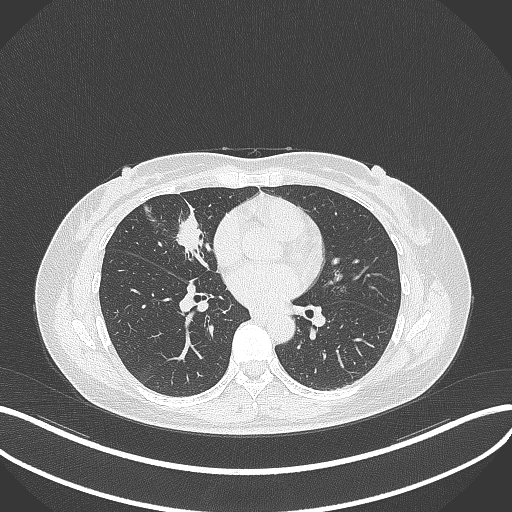
Chest CT, one axial slice; slice 139 of 284 in the series (ordered by position); reconstruction kernel B70f; lung window (W 1500 / L -600 HU); 512 × 512 image matrix, field of view 400 × 400 mm. Patient: female, 43 years. Case-level facts recorded for this patient, not image findings: clinical TNM (as recorded): T1c N3 M1; histopathological grade: G1.
Annotated regions visible in this slice (bounding box drawn by a radiologist):
- lung tumour (recorded histology: adenocarcinoma): bounding box [x1, y1, x2, y2] px = [171, 210, 206, 261]